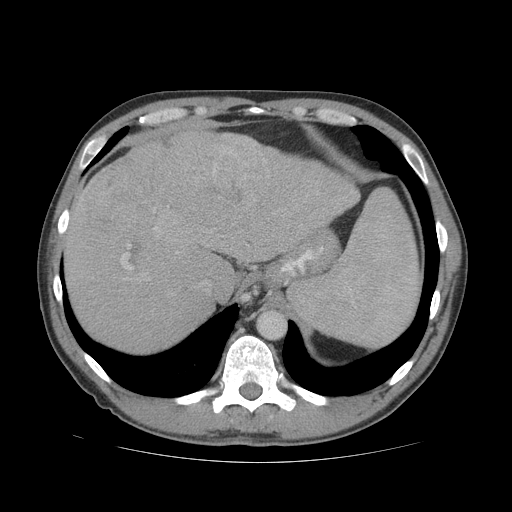
Contrast-enhanced abdominal CT (liver protocol), one axial slice. Slice 56 of 81 in the series (ordered by position). Reconstruction kernel STANDARD. Soft-tissue window (W 400 / L 40 HU). 2.5 mm slice thickness. 512 × 512 image matrix, field of view 400 × 400 mm. From the clinical record (not read from this slice): diagnosis: hepatocellular carcinoma (patient treated with transarterial chemoembolisation; whether this scan precedes or follows treatment is not stated here); TNM stage (as recorded): Stage-IVB; Child-Pugh class: B; tumour differentiation: well differentiated; tumour nodularity: multinodular.
Annotated regions visible in this slice (semi-automatically segmented with operator editing):
- abdominal aorta: bounding box <258,312,285,339> (left, top, right, bottom; pixels)
- liver parenchyma outside the tumour (the mass and vessels are separate outlines, so this box may not span the whole liver): <64,130,360,352>
- mass: <76,129,269,234>
- liver vessels: <121,195,308,270>